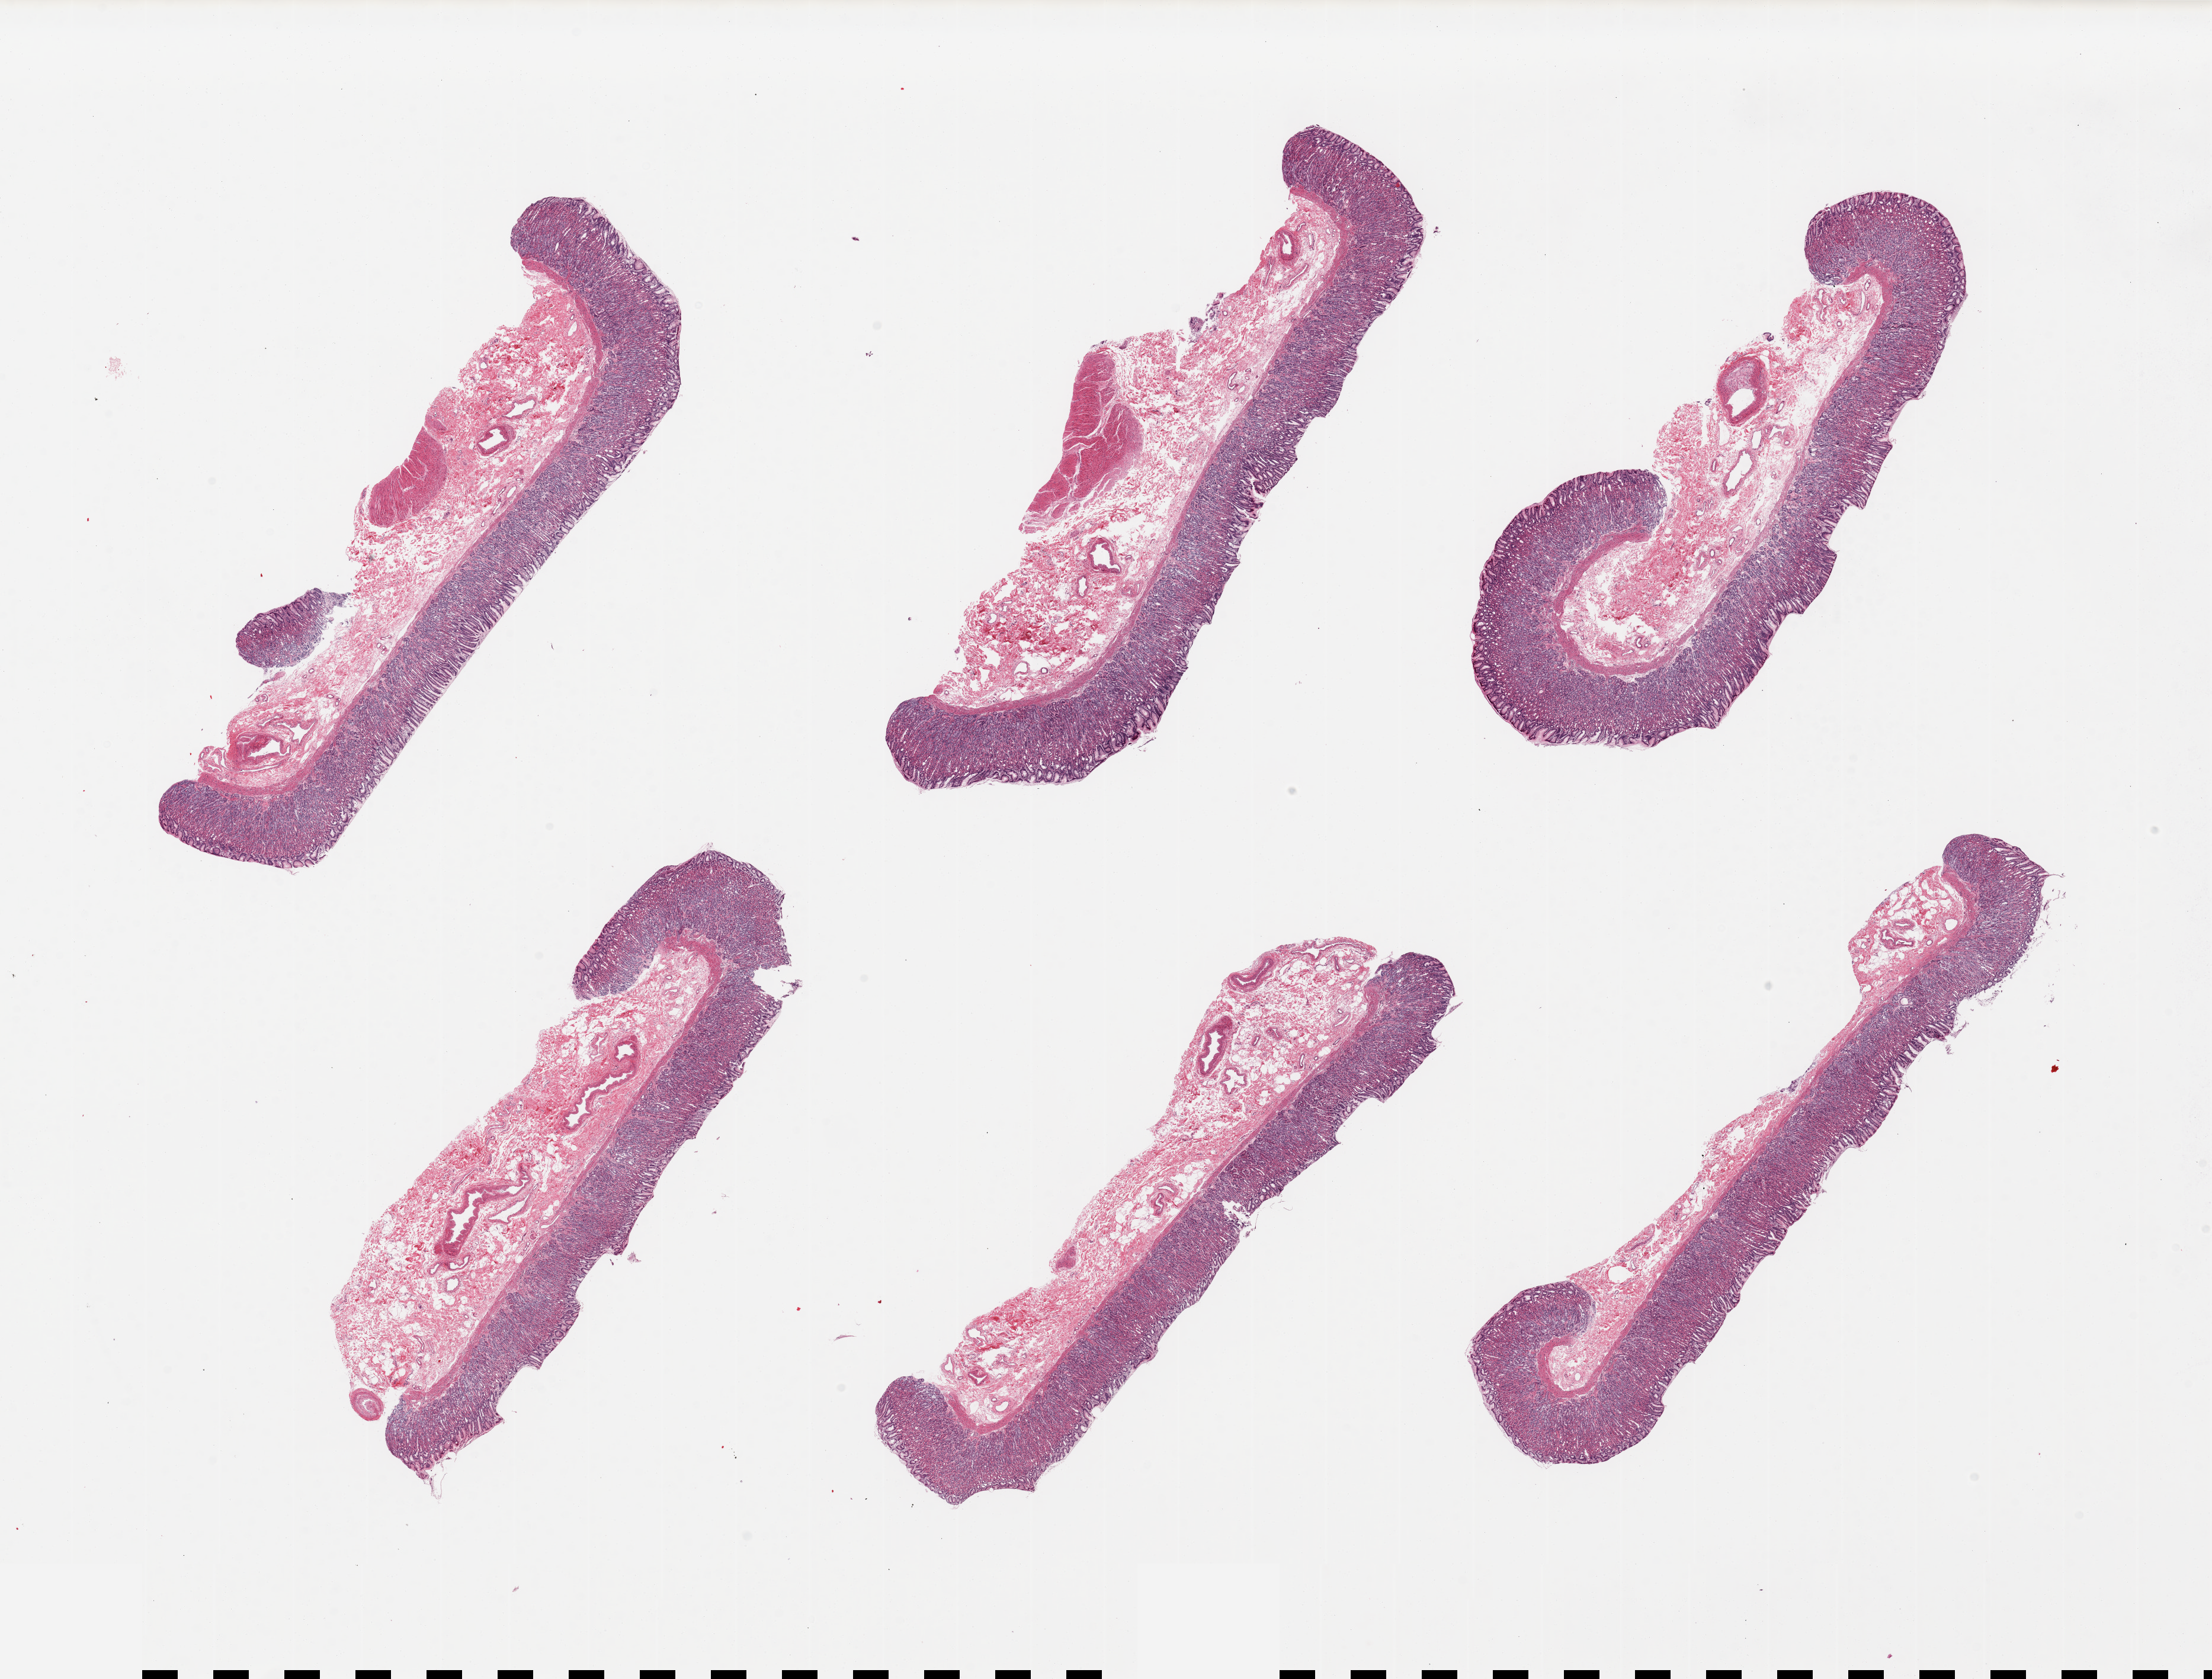
Whole-slide image, H&E stain, brightfield — low-resolution overview of the scanned area, about 29.5 x 22.4 mm, PAXgene-fixed paraffin-embedded (PFPE) section, sampled site (target tissue): stomach, donor tissue sample. Donor sex: female.
Review note (as recorded): 6 pieces, mucosa well preserved, up to ~1mm thick, ~40 % thickness.